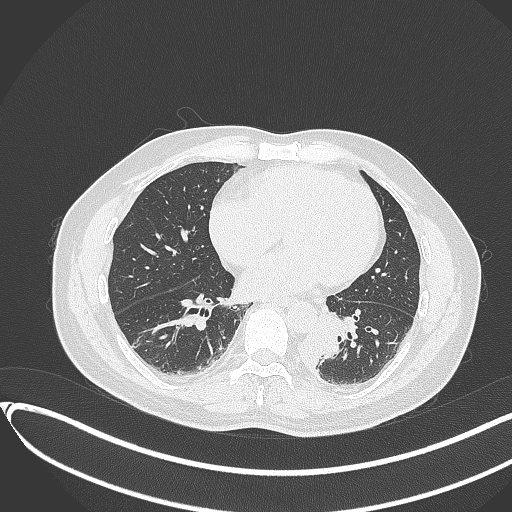
Chest CT, one axial slice. Slice 130 of 417 in the series (ordered by position). Reconstruction kernel B70f. 120 kVp. Lung window (W 1500 / L -600 HU). 512 × 512 image matrix, field of view 400 × 400 mm. Patient: male, 54 years. Case-level facts recorded for this patient, not image findings: clinical TNM (as recorded): T3 N0 M0.
Outlined on this slice (bounding box drawn by a radiologist):
- lung tumour (recorded histology: squamous cell carcinoma): bounding box [x1, y1, x2, y2] px = [293, 307, 343, 375]